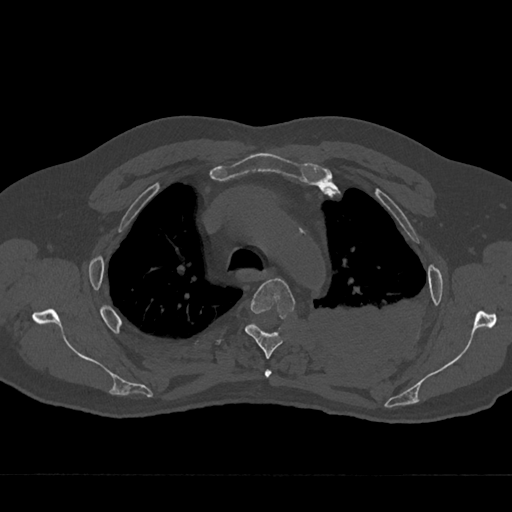
CT including the spine, one axial slice. Slice 519 of 797 in the series (ordered by position). Bone window (W 1800 / L 400 HU). 512 × 512 image matrix, field of view 377 × 377 mm. Male patient, age 75 years. Case-level facts recorded for this patient, not image findings: primary cancer: renal.
Structures marked on this image (semi-automatically segmented with operator editing):
- T3 vertebra: bounding box [x1, y1, x2, y2] px = [264, 370, 272, 378]
- T4 vertebra: [245, 278, 295, 359]
- T5 vertebra: [252, 324, 257, 327]